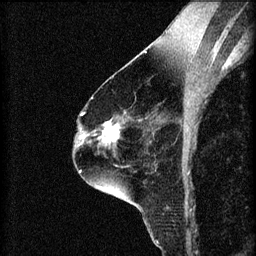
Breast MRI (dynamic contrast-enhanced), one sagittal slice. Slice 40 of 60 in the series (ordered by position). 3 images stored at this slice position (order not interpretable as contrast timing). 1.5 T. TE 4.2 ms, TR 8.2 ms. 2 mm slice thickness. 256 × 256 image matrix, field of view 180 × 180 mm. Patient: female, 60 years.
Annotated regions visible in this slice (semi-automatic segmentation, software-assisted and operator-edited):
- analysis volume of interest (the breast-tissue region the enhancement analysis was run in; not a lesion): bounding box (x1, y1, x2, y2) in pixels: (89, 116, 125, 151)
- tumour enhancement mask (voxels above the 70 % enhancement threshold inside the analysis volume of interest): (95, 122, 120, 143)